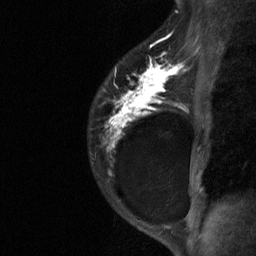
Breast MRI (dynamic contrast-enhanced), one sagittal slice. Slice 48 of 64 in the series (ordered by position). Dynamic contrast-enhanced study with each time point stored as its own series, time point 2 of 3 at this slice position (early post-contrast, ordered by acquisition time). 1.5 T. TE 4.8 ms, TR 27 ms. 2 mm slice thickness. 256 × 256 image matrix, field of view 180 × 180 mm. Female patient, age 34 years. From the clinical record (not read from this slice): setting: breast cancer imaged before/during neoadjuvant chemotherapy; receptor status: HR-positive, HER2-negative.
Structures marked on this image (semi-automatically segmented with operator editing):
- analysis volume of interest (the breast-tissue region the enhancement analysis was run in; not a lesion): bounding box [x1, y1, x2, y2] px = [88, 44, 181, 191]
- tumour enhancement mask (voxels above the 90 % enhancement threshold inside the analysis volume of interest): [104, 45, 181, 151]